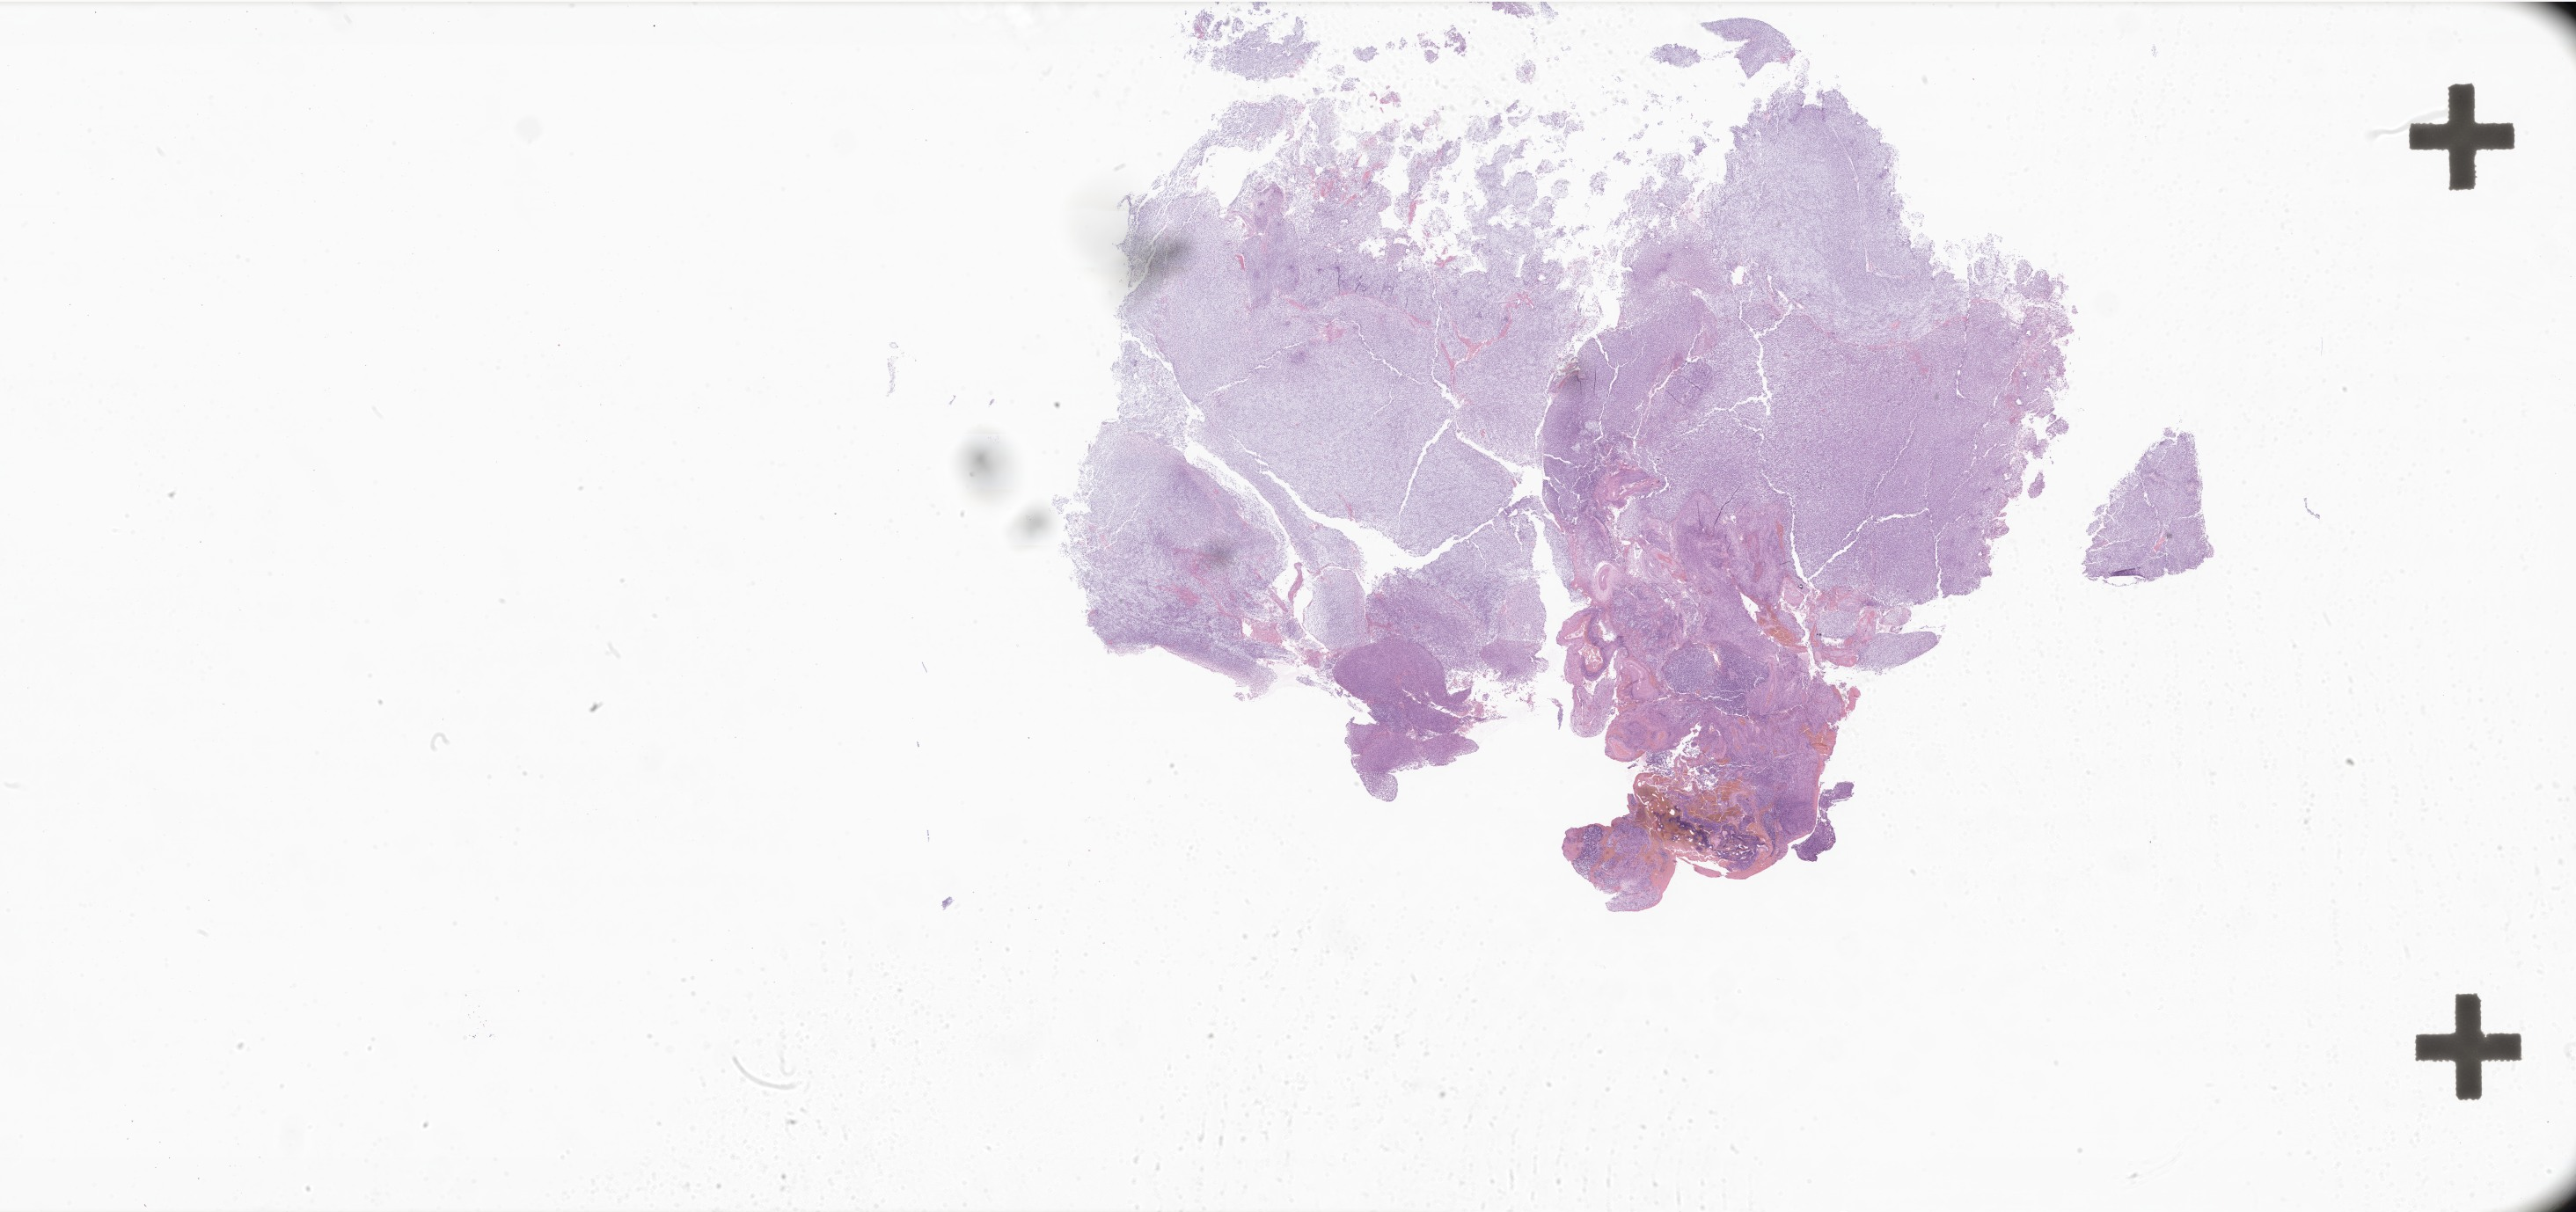
H&E whole-slide image of tumor tissue from the brain — shown as a low-resolution overview of the whole scanned area (about 49.4 x 23.2 mm); formalin-fixed paraffin-embedded section. Female patient, age 434 days (about 1.2 years).
Diagnosis: Tumor cells, uncertain whether benign or malignant.